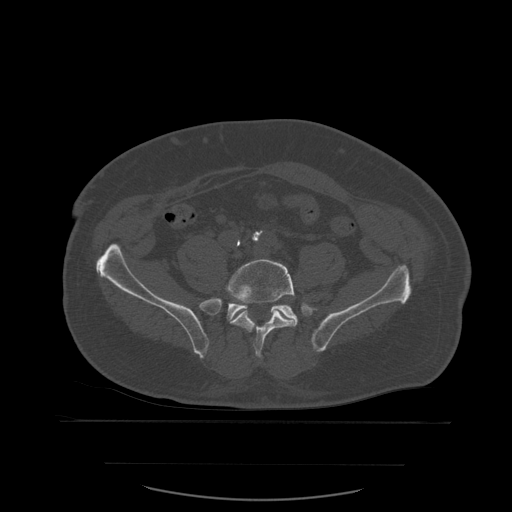
CT including the spine, one axial slice. Position 132 of 590 along the scan axis. Bone window (W 1800 / L 400 HU). 512 × 512 image matrix. Patient age 71 years. From the clinical record (not read from this slice): primary cancer: lung; vertebrae with lytic lesions (as recorded): T1, T2, L5, S1.
Outlined on this slice (semi-automatically segmented with operator editing):
- L5 vertebra: bounding box <227,259,297,358> (left, top, right, bottom; pixels)